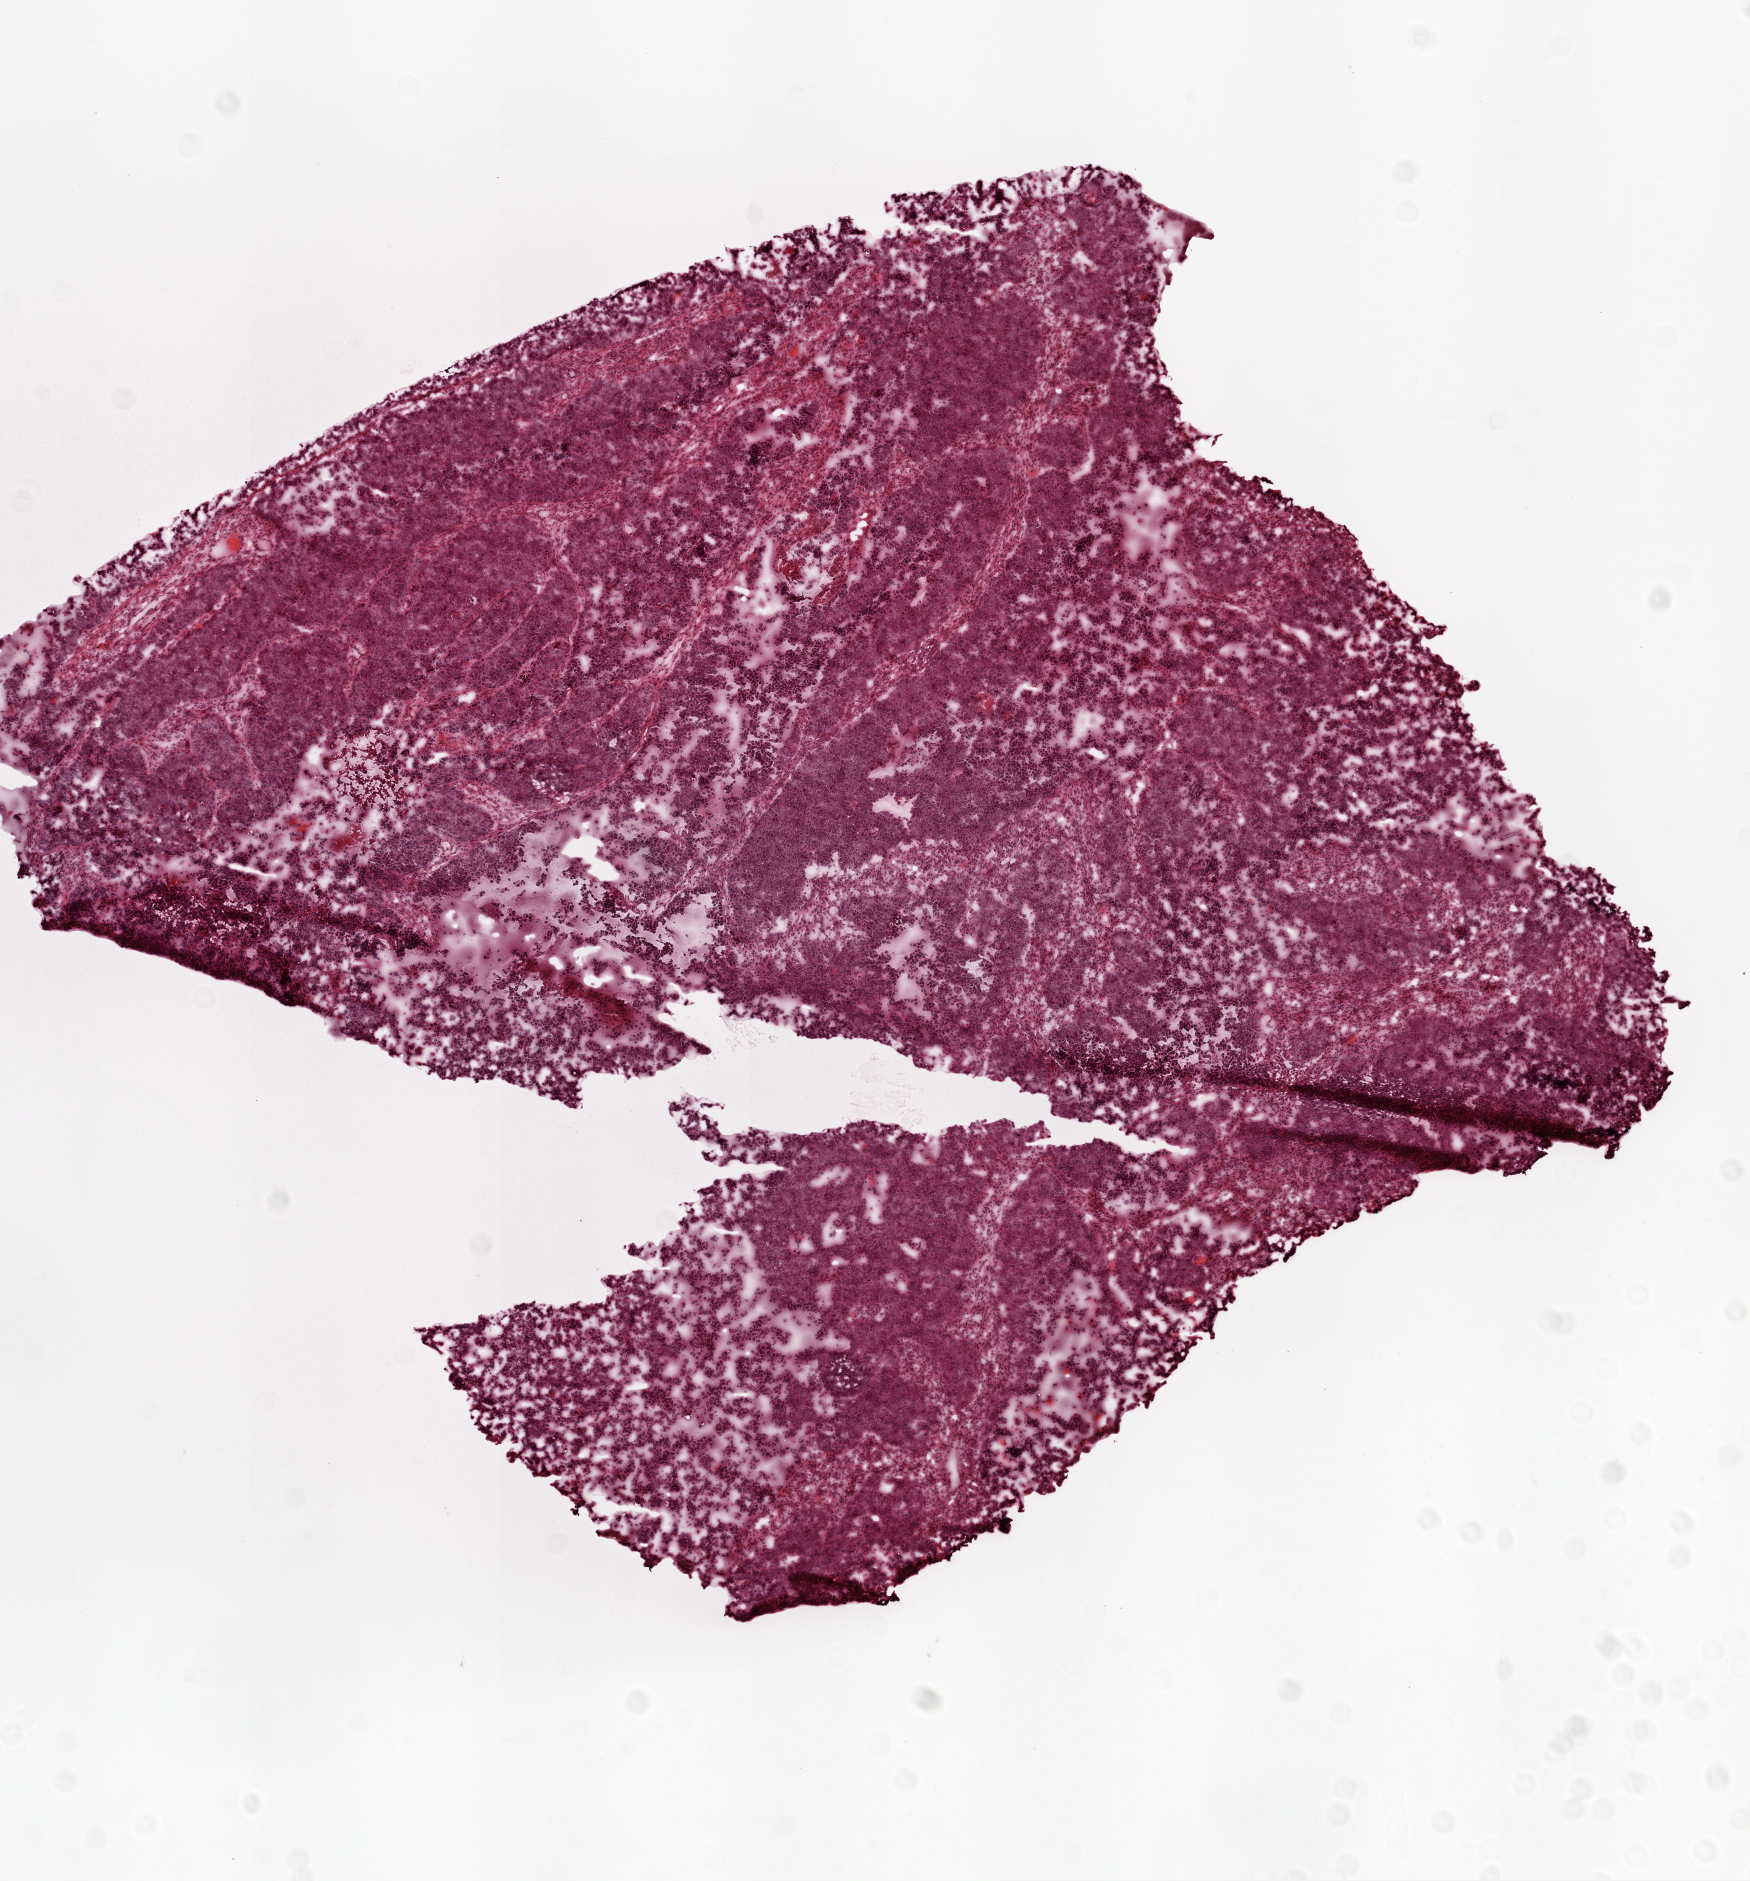
Whole-slide histology image, H&E — a low-resolution overview of the entire scanned area, about 7.0 x 7.5 mm; frozen section from the top of the tissue portion; sample: primary tumour, ovary. Female, age 55 years at initial diagnosis. Histologic grade: G3 (poorly differentiated). Slide review estimates, as recorded: tumour cells 80%, tumour nuclei 95%, normal cells 0%, stromal cells 20%, necrosis 0%.
FIGO stage: IIIC. Laterality: bilateral. Histologic diagnosis: Serous surface papillary carcinoma.